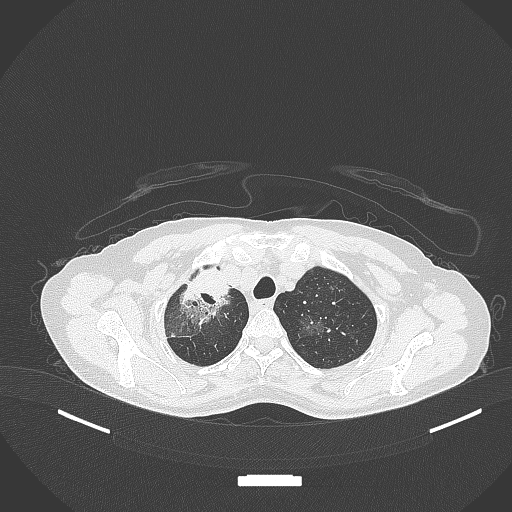
Chest CT, one axial slice; slice 276 of 284 in the series (ordered by position); reconstruction kernel B70f; 120 kVp; lung window (W 1500 / L -600 HU); 1 mm slice thickness; 512 × 512 image matrix, field of view 400 × 400 mm. Female patient, age 59 years. From the clinical record (not read from this slice): clinical TNM (as recorded): T3 N0 M0; histopathological grade: G1.
Structures marked on this image (bounding box drawn by a radiologist):
- lung tumour (recorded histology: adenocarcinoma): box from (x=173, y=264) to (x=231, y=328) px